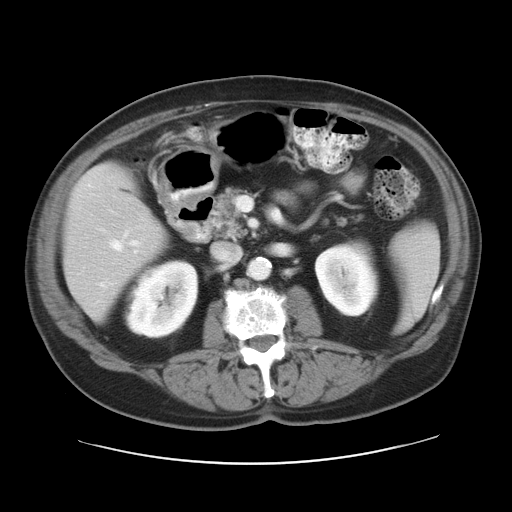
Contrast-enhanced abdominal CT, one axial slice. Slice 13 of 28 in the series (ordered by position). Reconstruction kernel STANDARD. Soft-tissue window (W 400 / L 40 HU). 512 × 512 image matrix, field of view 402 × 402 mm. Male patient, age 74 years. From the clinical record (not read from this slice): diagnosis: colorectal cancer liver metastases, imaged before liver resection; multiple liver metastases: no; largest metastasis: 5 cm; disease in both lobes: no.
Outlined on this slice (manually delineated by an expert):
- hepatic veins: bounding box (x1, y1, x2, y2) in pixels: (99, 240, 140, 287)
- liver: (63, 167, 164, 318)
- planned liver remnant (the part of the liver to remain after resection): (63, 168, 165, 319)